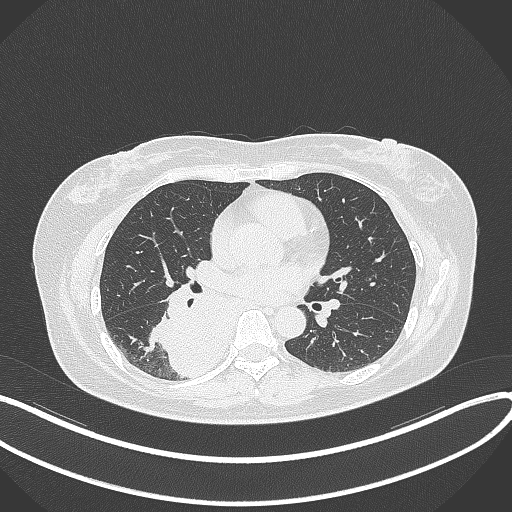
Chest CT, one axial slice; position 182 of 331 along the scan axis; reconstruction kernel B70f; 120 kVp; lung window (W 1500 / L -600 HU); 512 × 512 image matrix, field of view 400 × 400 mm. Female patient, age 54 years. From the clinical record (not read from this slice): clinical TNM (as recorded): T4 N0 M0.
Annotated regions visible in this slice (bounding box drawn by a radiologist):
- lung tumour (recorded histology: adenocarcinoma): bounding box (x1, y1, x2, y2) in pixels: (151, 285, 237, 379)